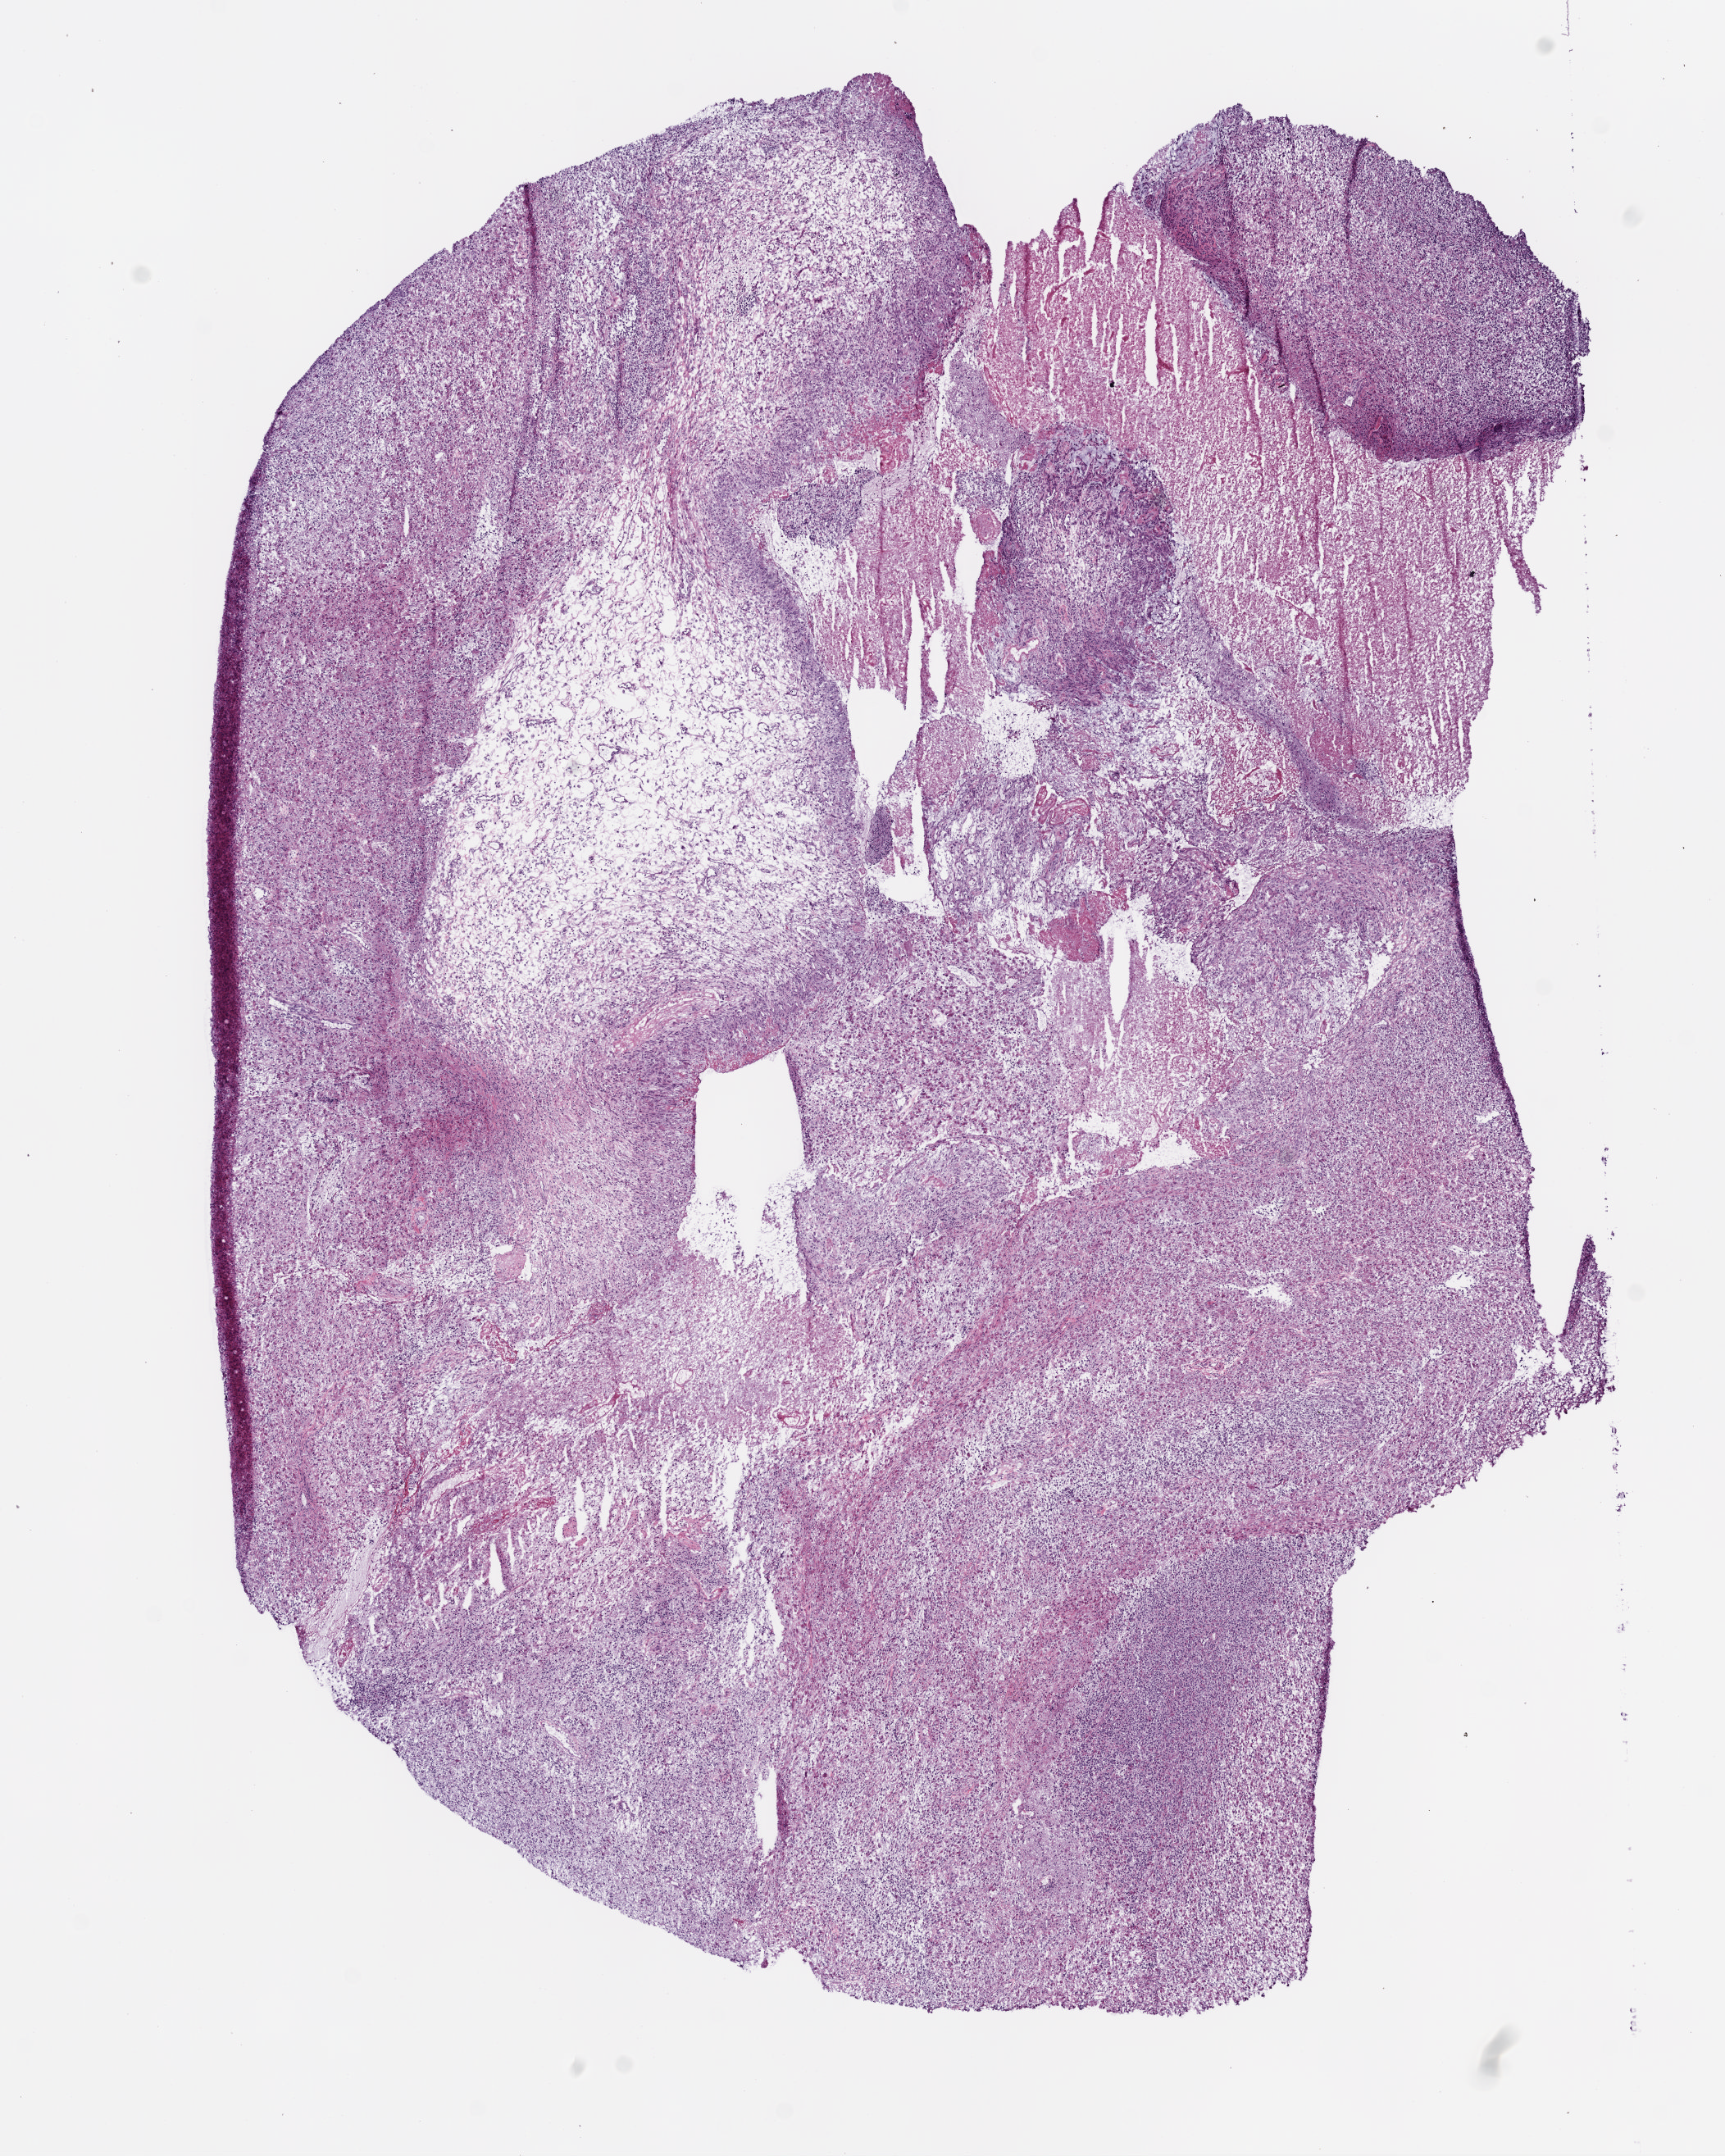
H&E whole-slide image — shown as a low-resolution overview of the whole scanned area (about 8.4 x 10.5 mm, slide scanned at 5x); frozen section; primary tumour sample from the brain. Patient: male, age at initial diagnosis 67 years. Slide review estimates, as recorded: tumour cells 85%, tumour nuclei 85%, normal cells 0%, stromal cells 0%, necrosis 15%.
* pathologic diagnosis: Glioblastoma